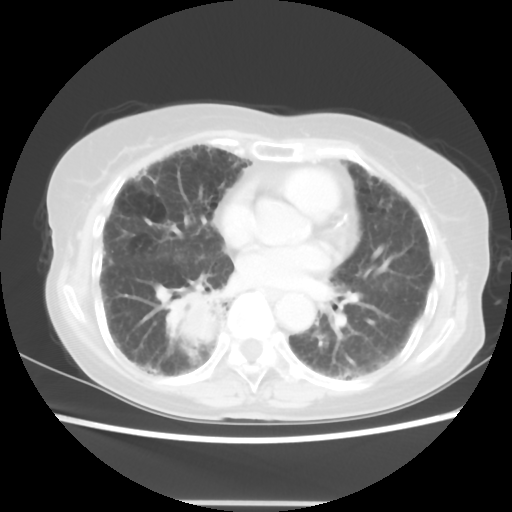
Chest CT, one axial slice; reconstruction kernel STANDARD; 120 kVp; lung window (W 1500 / L -600 HU); 5 mm slice thickness; 512 × 512 image matrix, field of view 325 × 325 mm. Patient: female, 71 years. Case-level facts recorded for this patient, not image findings: clinical TNM (as recorded): T3 N0 M0.
Annotated regions visible in this slice (bounding box drawn by a radiologist):
- lung tumour (recorded histology: squamous cell carcinoma): bounding box [x1, y1, x2, y2] px = [170, 289, 227, 348]